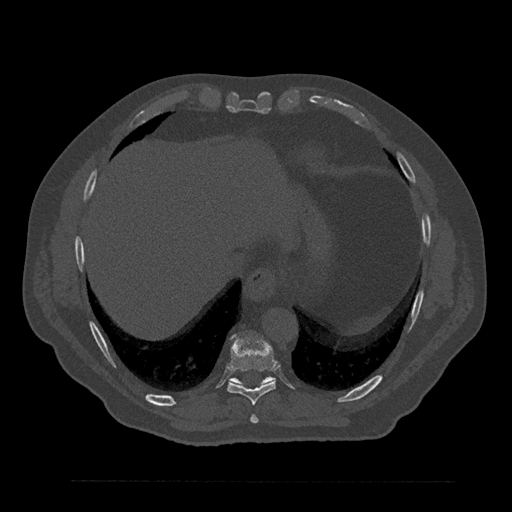
CT including the spine, one axial slice. Slice 392 of 797 in the series (ordered by position). Reconstruction kernel Br40s/3. 120 kVp. Bone window (W 1800 / L 400 HU). 0.5 mm slice thickness. 512 × 512 image matrix, field of view 430 × 430 mm. Patient: male, 61 years. Case-level facts recorded for this patient, not image findings: primary cancer: prostate.
Outlined on this slice (semi-automatic segmentation, software-assisted and operator-edited):
- T10 vertebra: box from (x=230, y=377) to (x=274, y=386) px
- T8 vertebra: (x=250, y=415)–(x=259, y=424)
- T9 vertebra: (x=227, y=335)–(x=277, y=405)